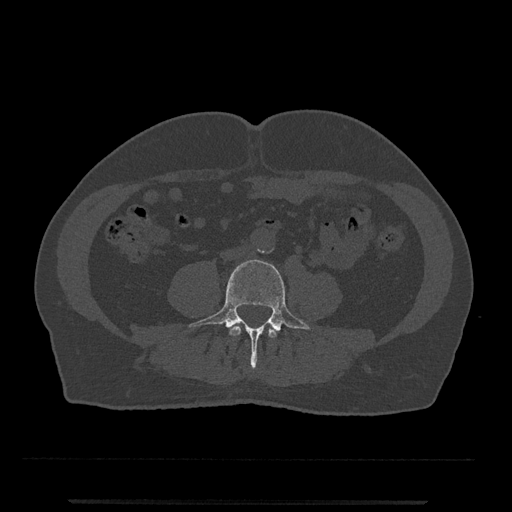
CT including the spine, one axial slice; position 146 of 797 along the scan axis; reconstruction kernel Br40s/3; bone window (W 1800 / L 400 HU); 0.5 mm slice thickness; 512 × 512 image matrix. Male patient, age 63 years. From the clinical record (not read from this slice): primary cancer: prostate.
Structures marked on this image (semi-automatic segmentation, software-assisted and operator-edited):
- L3 vertebra: bounding box [x1, y1, x2, y2] px = [229, 325, 277, 338]
- L4 vertebra: [189, 259, 313, 369]